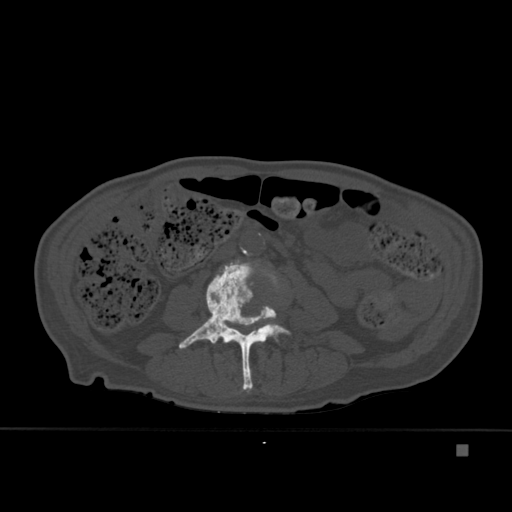
CT including the spine, one axial slice; slice 141 of 451 in the series (ordered by position); bone window (W 1800 / L 400 HU); 1.5 mm slice thickness; 512 × 512 image matrix, field of view 378 × 378 mm. Patient: male, 75 years. Case-level facts recorded for this patient, not image findings: primary cancer: prostate.
Annotated regions visible in this slice (semi-automatically segmented with operator editing):
- L3 vertebra: bounding box [x1, y1, x2, y2] px = [179, 259, 291, 393]